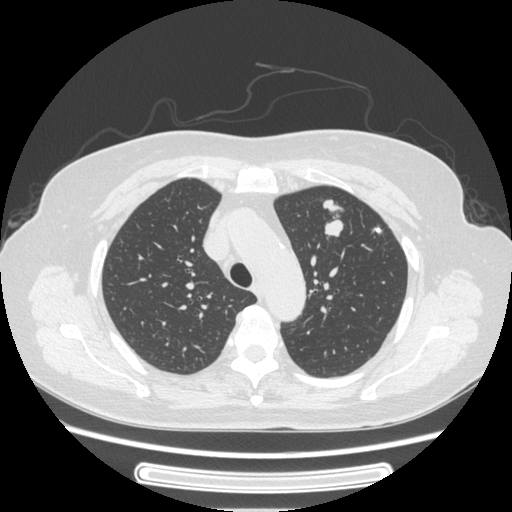
Chest CT, one axial slice; position 177 of 227 along the scan axis; 120 kVp; lung window (W 1500 / L -600 HU); 1.25 mm slice thickness; 512 × 512 image matrix. Female patient, age 77 years. From the clinical record (not read from this slice): clinical TNM (as recorded): T1c N3 M0.
Structures marked on this image (bounding box drawn by a radiologist):
- lung tumour (recorded histology: adenocarcinoma): bounding box (x1, y1, x2, y2) in pixels: (310, 192, 351, 253)